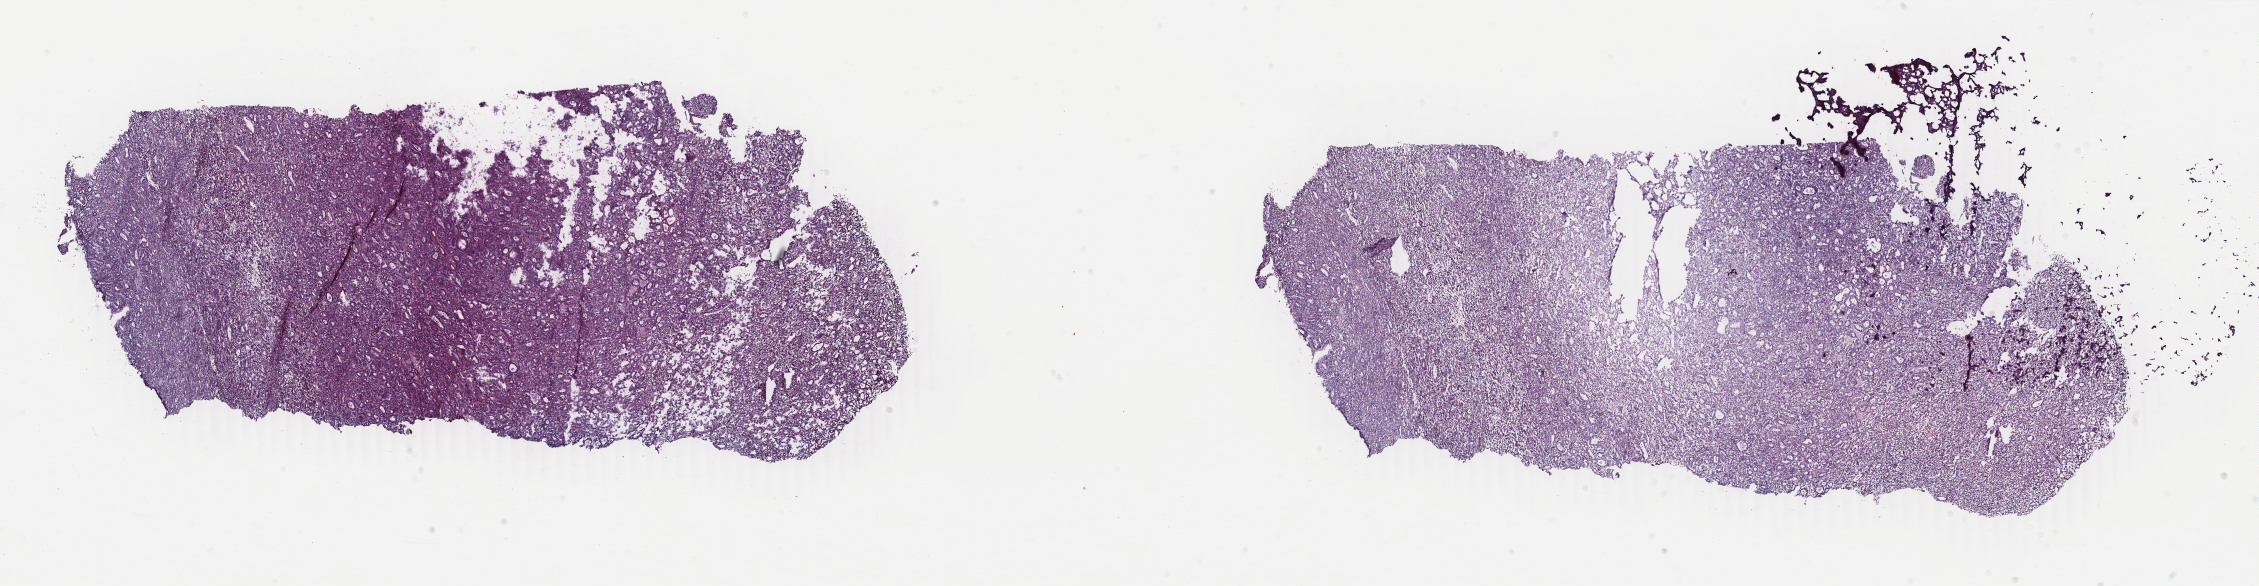
H&E-stained whole-slide image — shown as a low-resolution overview of the whole scanned area (about 35.9 x 9.3 mm, slide scanned at 40x). Frozen section. Uterus, primary tumour sample. Patient: female, age at initial diagnosis 64 years. Histologic grade: G2 (moderately differentiated). Pathologist review of this section (percent, as recorded): tumour cells 90%, tumour nuclei 85%, normal cells 0%, stromal cells 9%, necrosis 1%. Infiltration values recorded for this section: lymphocyte infiltration 7%, monocyte infiltration 5%, neutrophil infiltration 1%.
Pathologic diagnosis: Endometrioid adenocarcinoma, NOS. FIGO stage: IA.